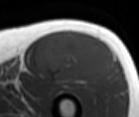
MRI of an extremity soft-tissue mass, one axial slice; slice 57 of 86 in the series (ordered by position); MR volume resampled by the dataset authors to the PET/CT grid (not the native acquisition matrix); 3.27 mm slice thickness; 139 × 117 image matrix. Male patient. From the clinical record (not read from this slice): histological type: extraskeletal osteosarcoma; grade: high; site of the primary tumour: thigh.
Annotated regions visible in this slice (expert contour drawn on MRI and transferred to this co-registered scan by the dataset authors):
- gross tumour volume (mass): box from (x=36, y=30) to (x=117, y=83) px